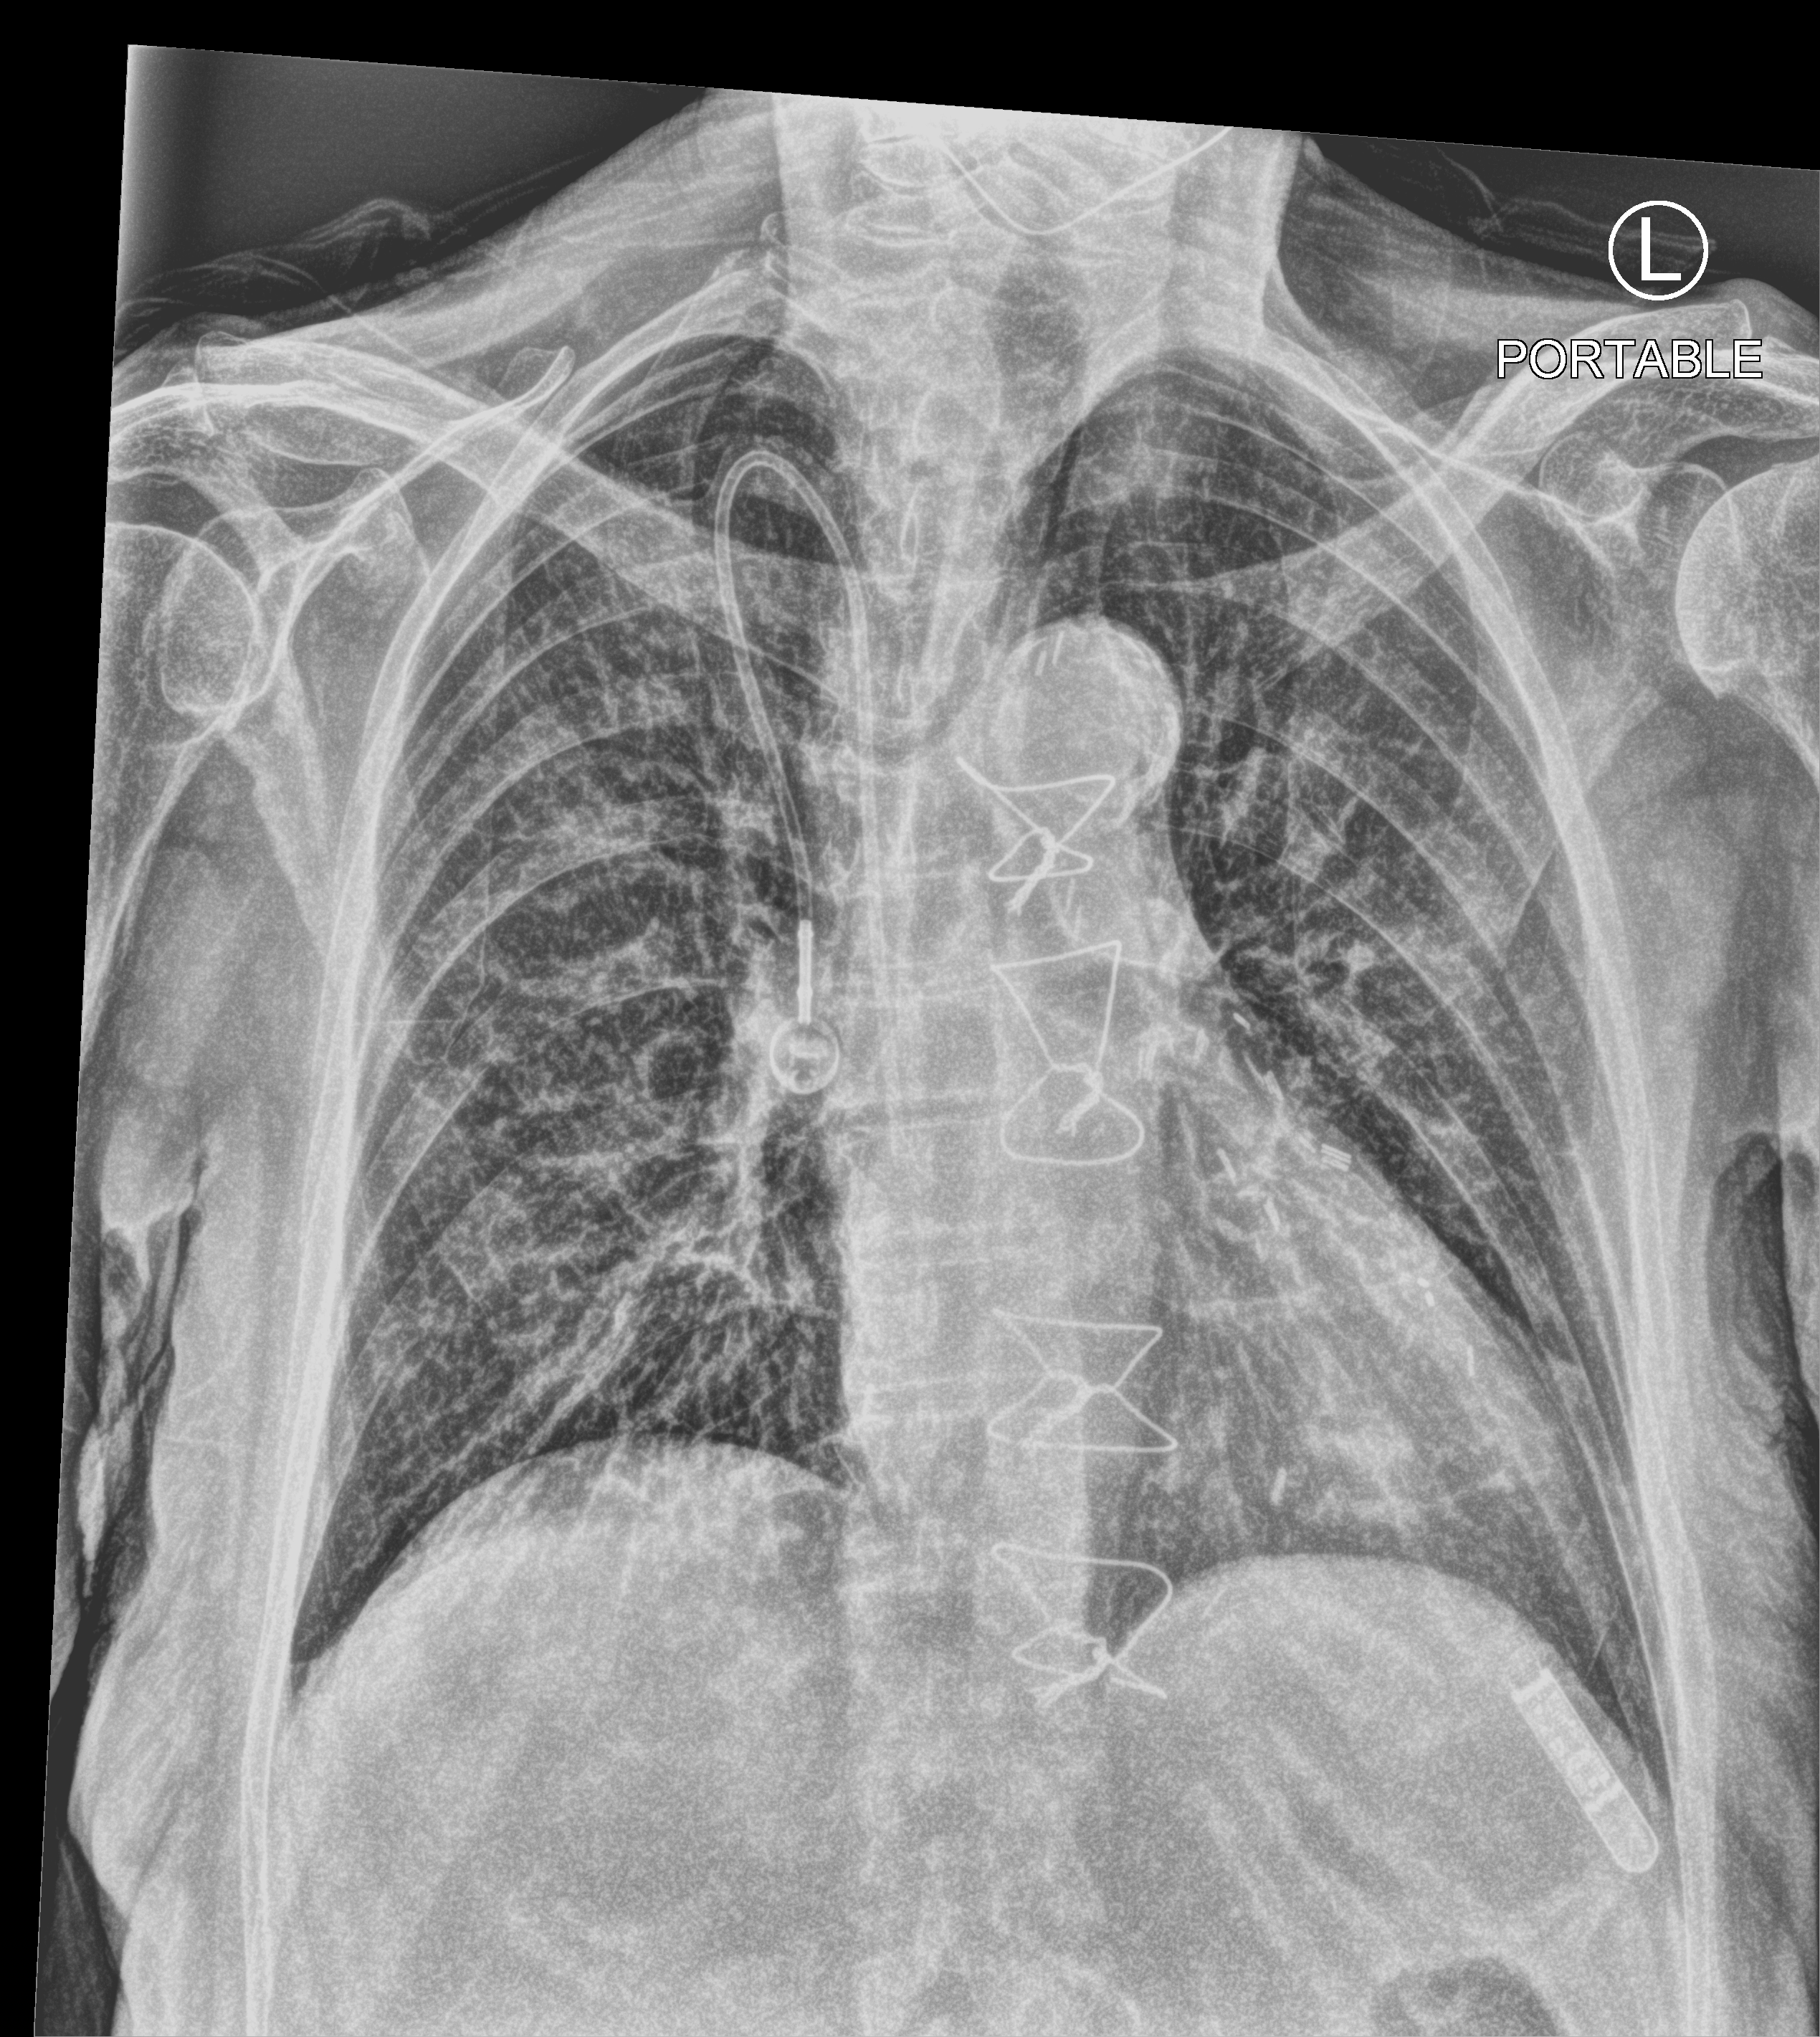
Bedside chest radiograph (computed radiography); anteroposterior (AP) projection. Female patient hospitalised with COVID-19, age 75–90 years.
From the hospital-stay record, not from the radiograph (when in the stay this image was taken is not recorded):
- mechanically ventilated during this hospital stay: no
- admitted to intensive care during this hospital stay: no